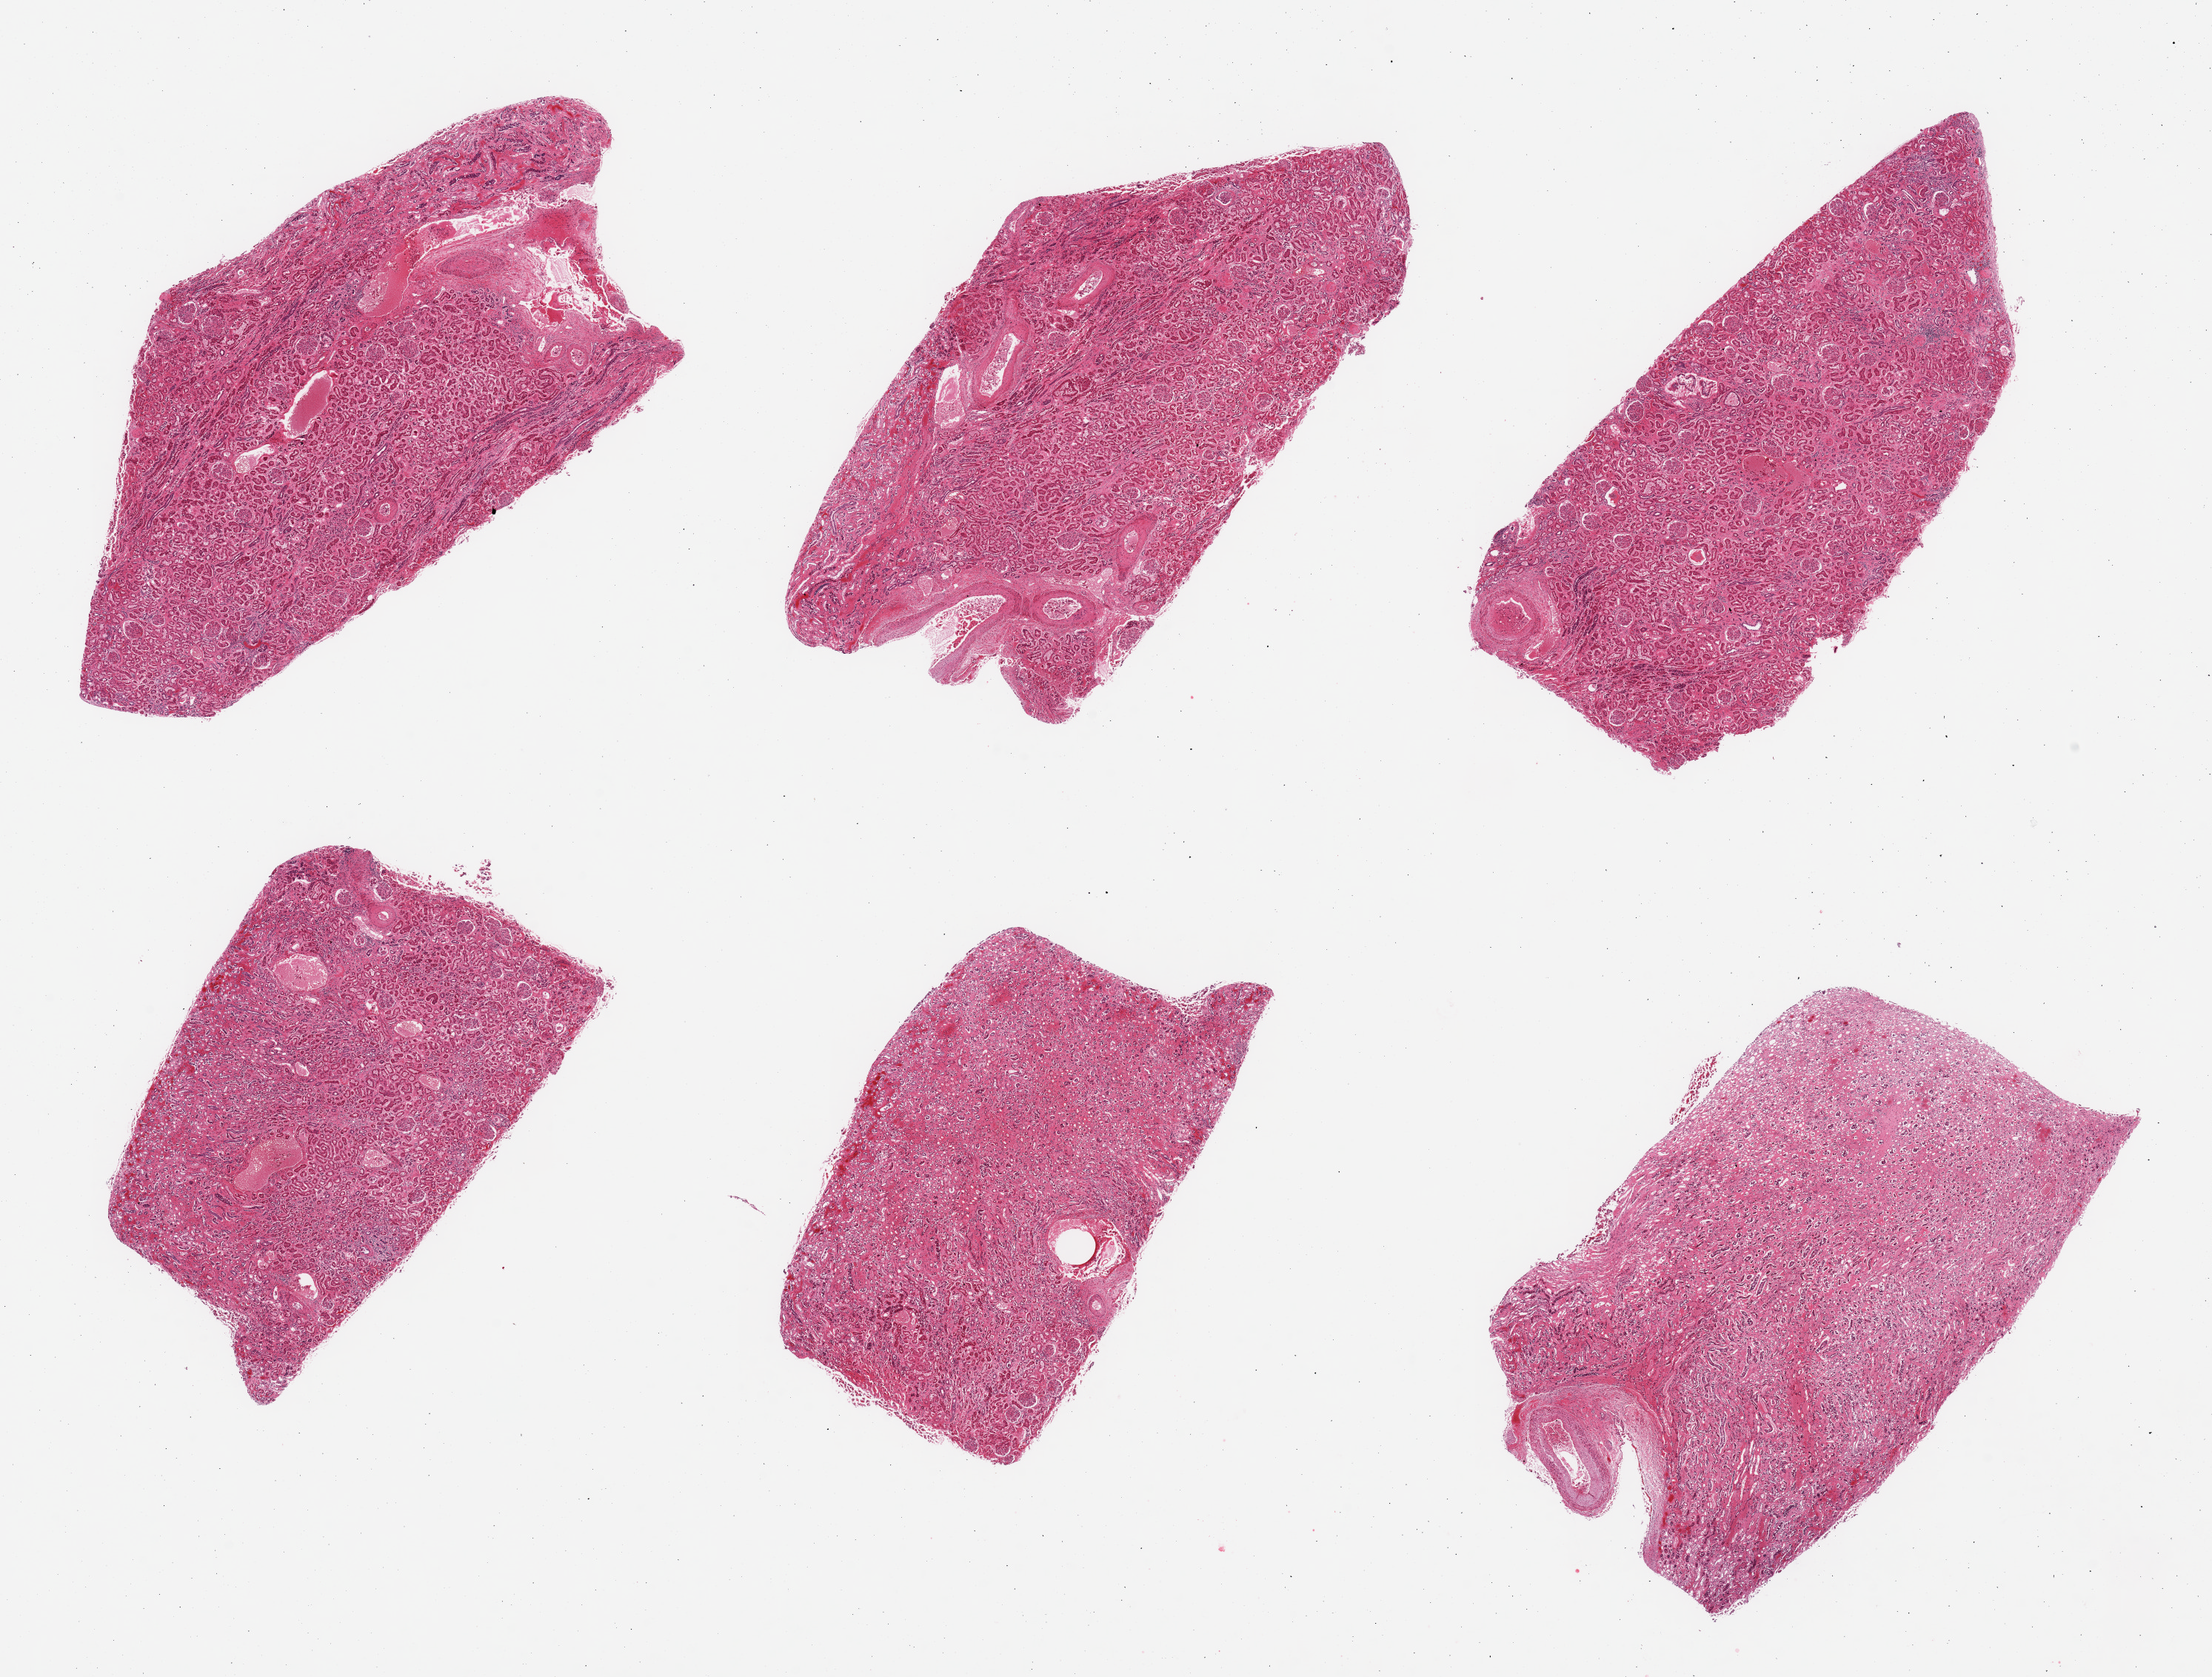
Whole-slide image, haematoxylin and eosin stain, brightfield, shown as a low-resolution overview of the whole scanned area (about 23.6 x 17.9 mm, from a 20x scan); PAXgene-fixed, paraffin-embedded tissue; target tissue: renal cortex; tissue donor sample. Donor: female.
Pathologist's review note for this sample: 6 pieces; 1 piece is medulla; another is largely medulla.